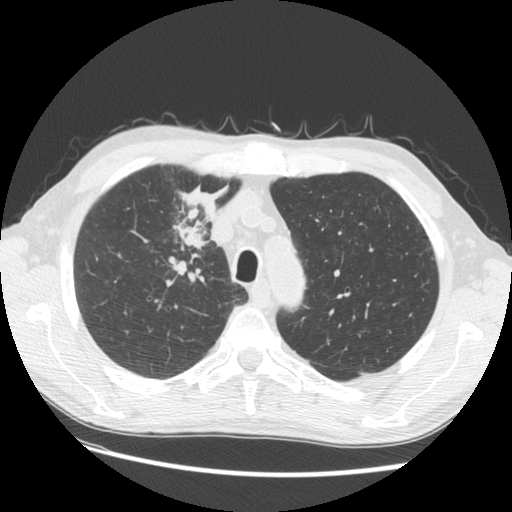
Axial slice from a low-dose chest CT screening exam. Third screening round (two years after baseline). Lung window (W 1500 / L -600 HU). Slice 30 of 133 in the series. Male participant, aged 73 years at enrolment. Current smoker at enrolment.
Lesion marked by an expert reader, bounding box [x1, y1, x2, y2] px = [142, 181, 232, 280]. The screening reader recorded 4 non-calcified nodules or masses ≥4 mm on this exam; which of them this box marks is not recorded. Official screen result: positive, other. Later outcome: lung cancer diagnosed 48 days after this screen — squamous cell carcinoma, NOS, right upper lobe, poorly differentiated (G3), stage IIIB (AJCC 6th edition), 56 mm at pathology.